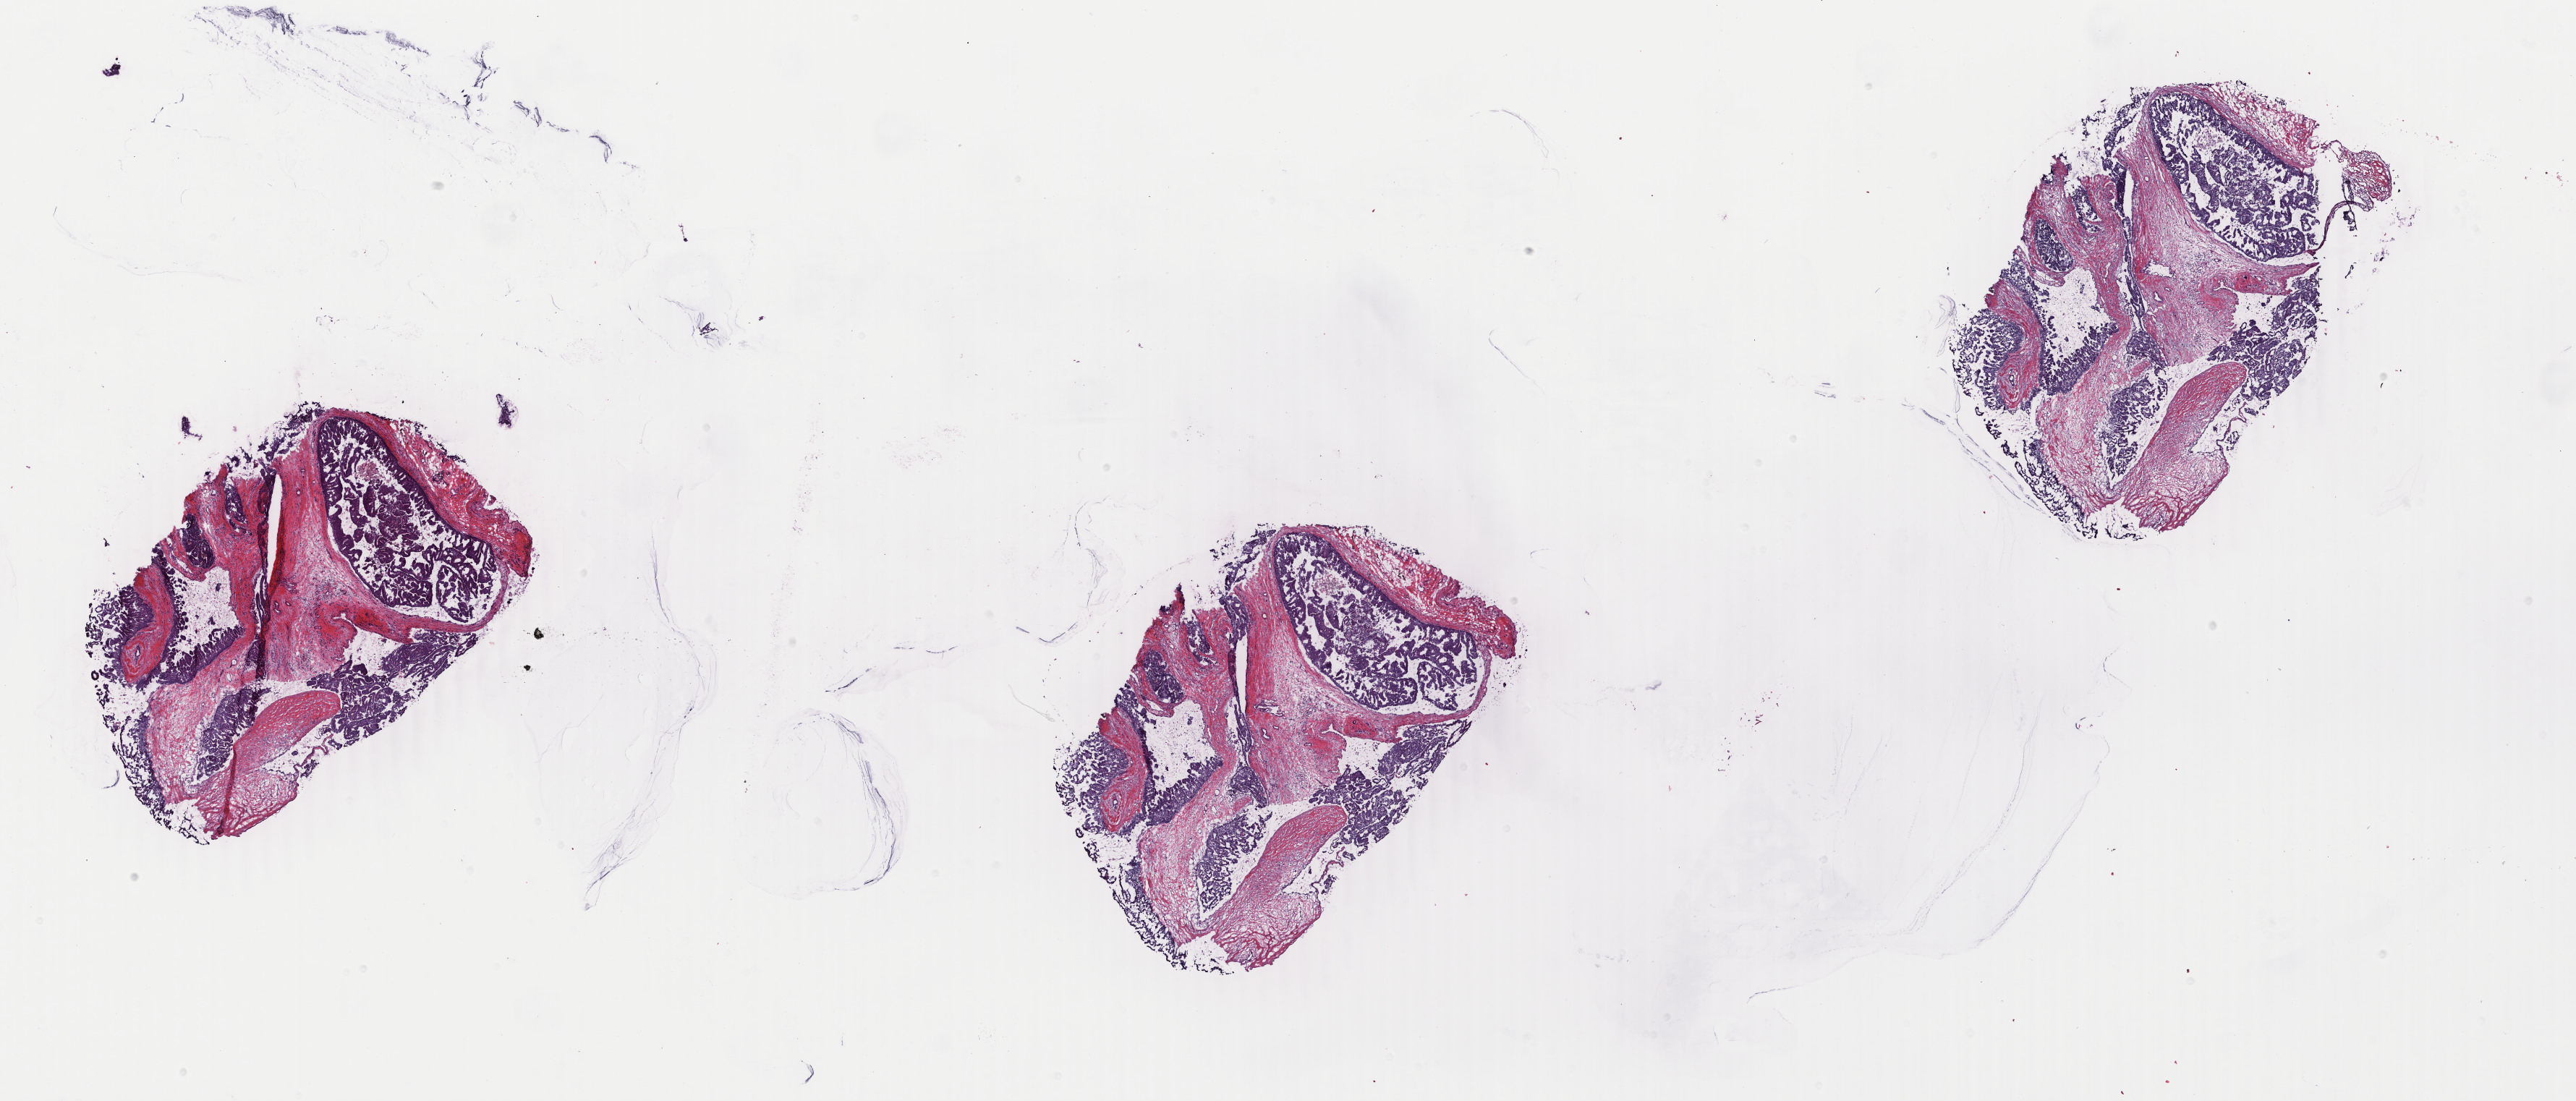
Whole-slide histology image, H&E-stained, shown as a low-resolution overview of the whole scanned area (about 28.3 x 12.1 mm, slide scanned at 40x); frozen section; sample: primary tumour, breast. Patient: female, age at initial diagnosis 63 years. Composition of this section per pathologist review: tumour cells 70%, tumour nuclei 70%, normal cells 0%, stromal cells 29%, necrosis 1%. Inflammatory infiltration, as recorded: lymphocyte infiltration 1%, monocyte infiltration 0%, neutrophil infiltration 0%.
AJCC pathologic stage: IA. Pathologic diagnosis: Infiltrating duct carcinoma, NOS.